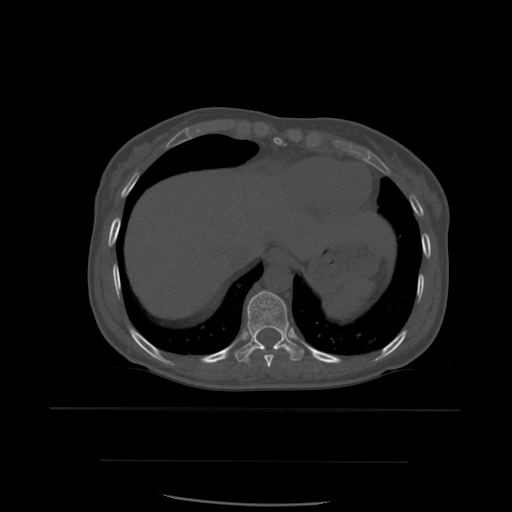
CT including the spine, one axial slice. Slice 322 of 574 in the series (ordered by position). Bone window (W 1800 / L 400 HU). 1.25 mm slice thickness. 512 × 512 image matrix, field of view 392 × 392 mm. Patient age 48 years. Case-level facts recorded for this patient, not image findings: primary cancer: lung.
Structures marked on this image (semi-automatically segmented with operator editing):
- T10 vertebra: box from (x=235, y=291) to (x=305, y=363) px
- T9 vertebra: (x=252, y=347)–(x=288, y=368)